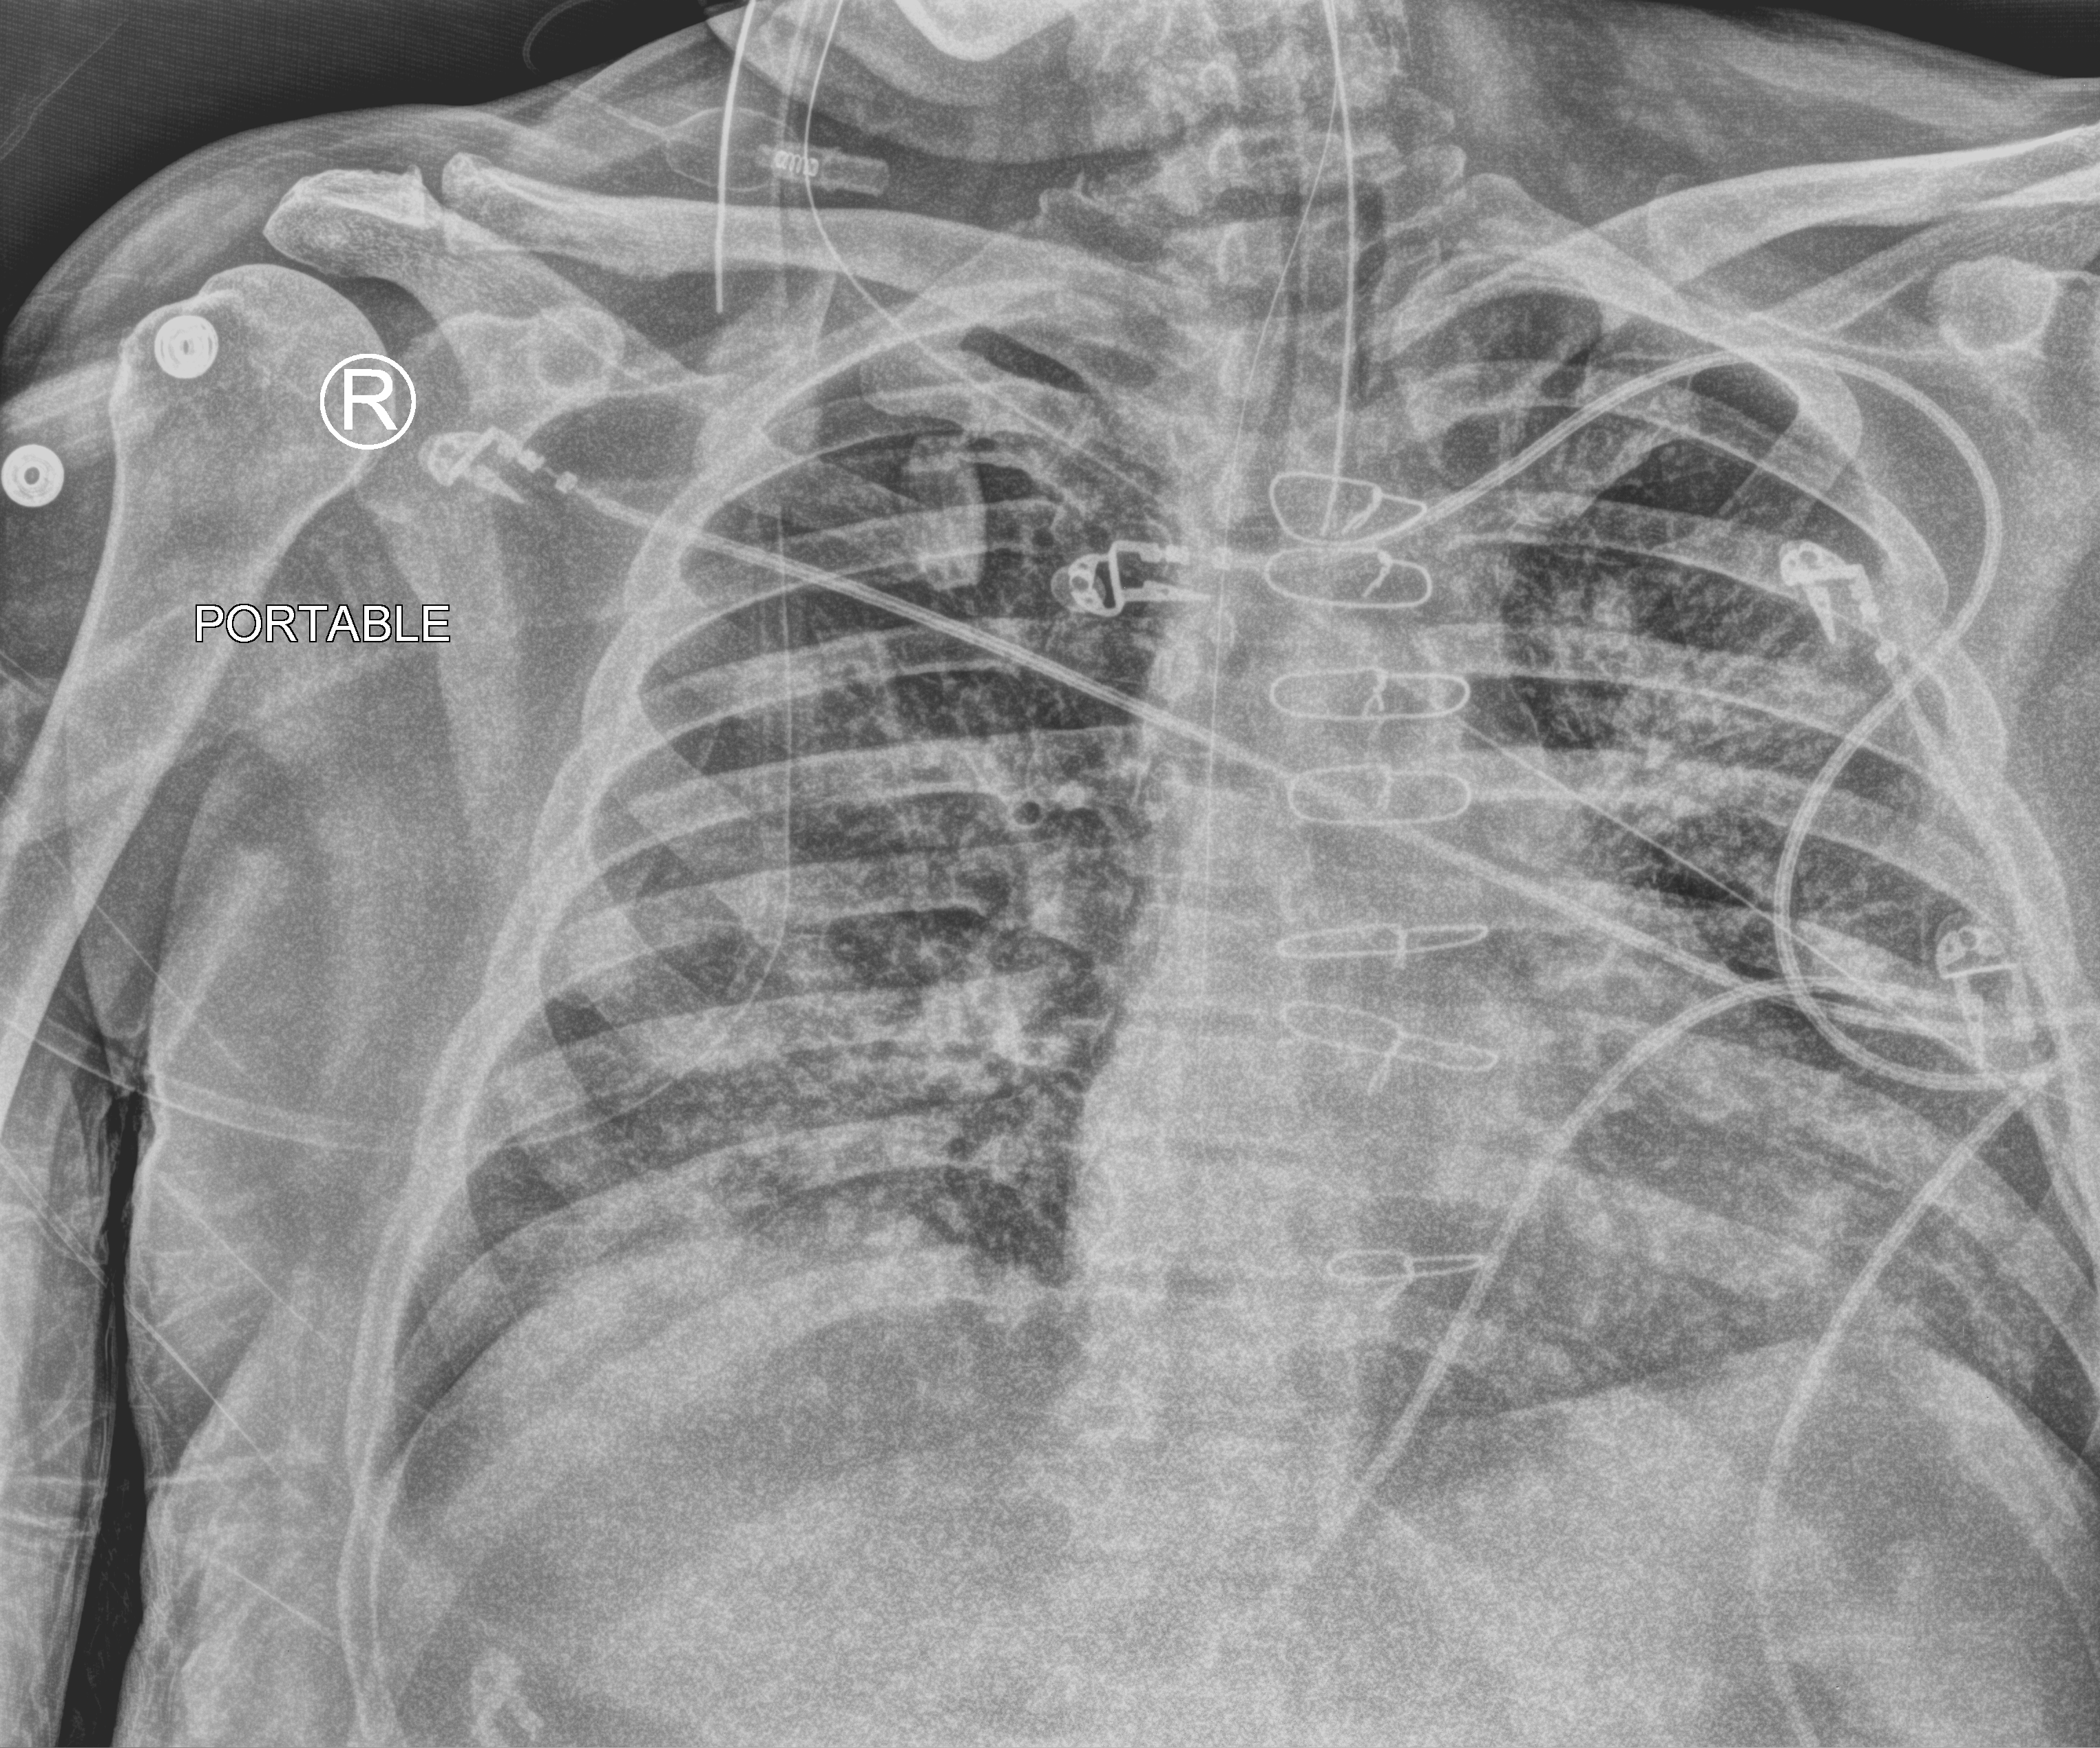
Bedside chest radiograph (computed radiography), anteroposterior (AP) projection. Patient hospitalised with COVID-19; male, aged 60–74 years.
From the hospital-stay record, not from the radiograph (when in the stay this image was taken is not recorded): COPD (admission record): no; mechanically ventilated during this hospital stay: yes.